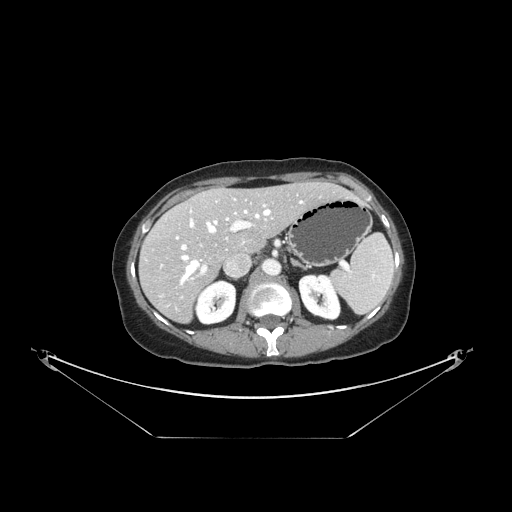
Contrast-enhanced abdominal CT, one axial slice. Slice 93 of 148 in the series (ordered by position). 120 kVp. Intravenous contrast given. Soft-tissue window (W 400 / L 40 HU). 2.5 mm slice thickness. 512 × 512 image matrix, field of view 500 × 500 mm. Female patient, age 73 years. Case-level facts recorded for this patient, not image findings: diagnosis: colorectal cancer liver metastases, imaged before liver resection; multiple liver metastases: no; largest metastasis: 1 cm; disease in both lobes: no.
Annotated regions visible in this slice (outlined manually by an expert reader):
- hepatic veins: box from (x=182, y=201) to (x=302, y=283) px
- liver: (x=139, y=182)–(x=351, y=321)
- planned liver remnant (the part of the liver to remain after resection): (x=168, y=183)–(x=351, y=255)
- portal vein (with intrahepatic branches): (x=176, y=204)–(x=266, y=275)